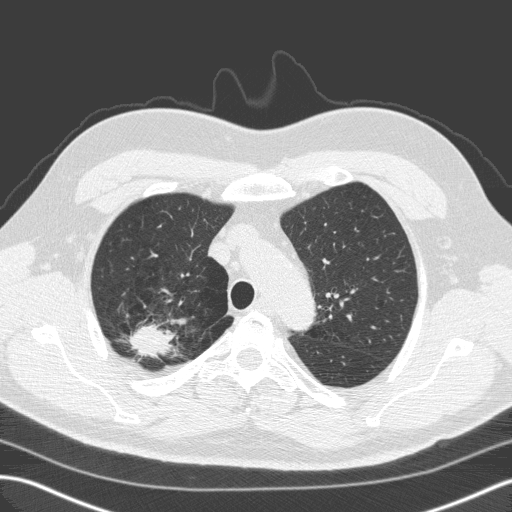
Axial slice from a low-dose chest CT screening exam. Baseline screening round. Lung window (W 1500 / L -600 HU). 2 mm slice thickness. Slice 30 of 149 in the series. Male participant, aged 59 years at enrolment.
• Expert reader's lesion annotation, bounding box [x1, y1, x2, y2] px = [118, 311, 179, 369].
• Screening reader's record for this exam (one nodule recorded; not confirmed to be the boxed lesion): non-calcified nodule or mass ≥4 mm, right upper lobe, 28 × 25 mm, spiculated (stellate) margins, soft tissue attenuation.
• Official screen result: positive, change unspecified: nodule(s) >= 4 mm or enlarging nodule(s), mass(es), or other non-specific abnormalities suspicious for lung cancer.